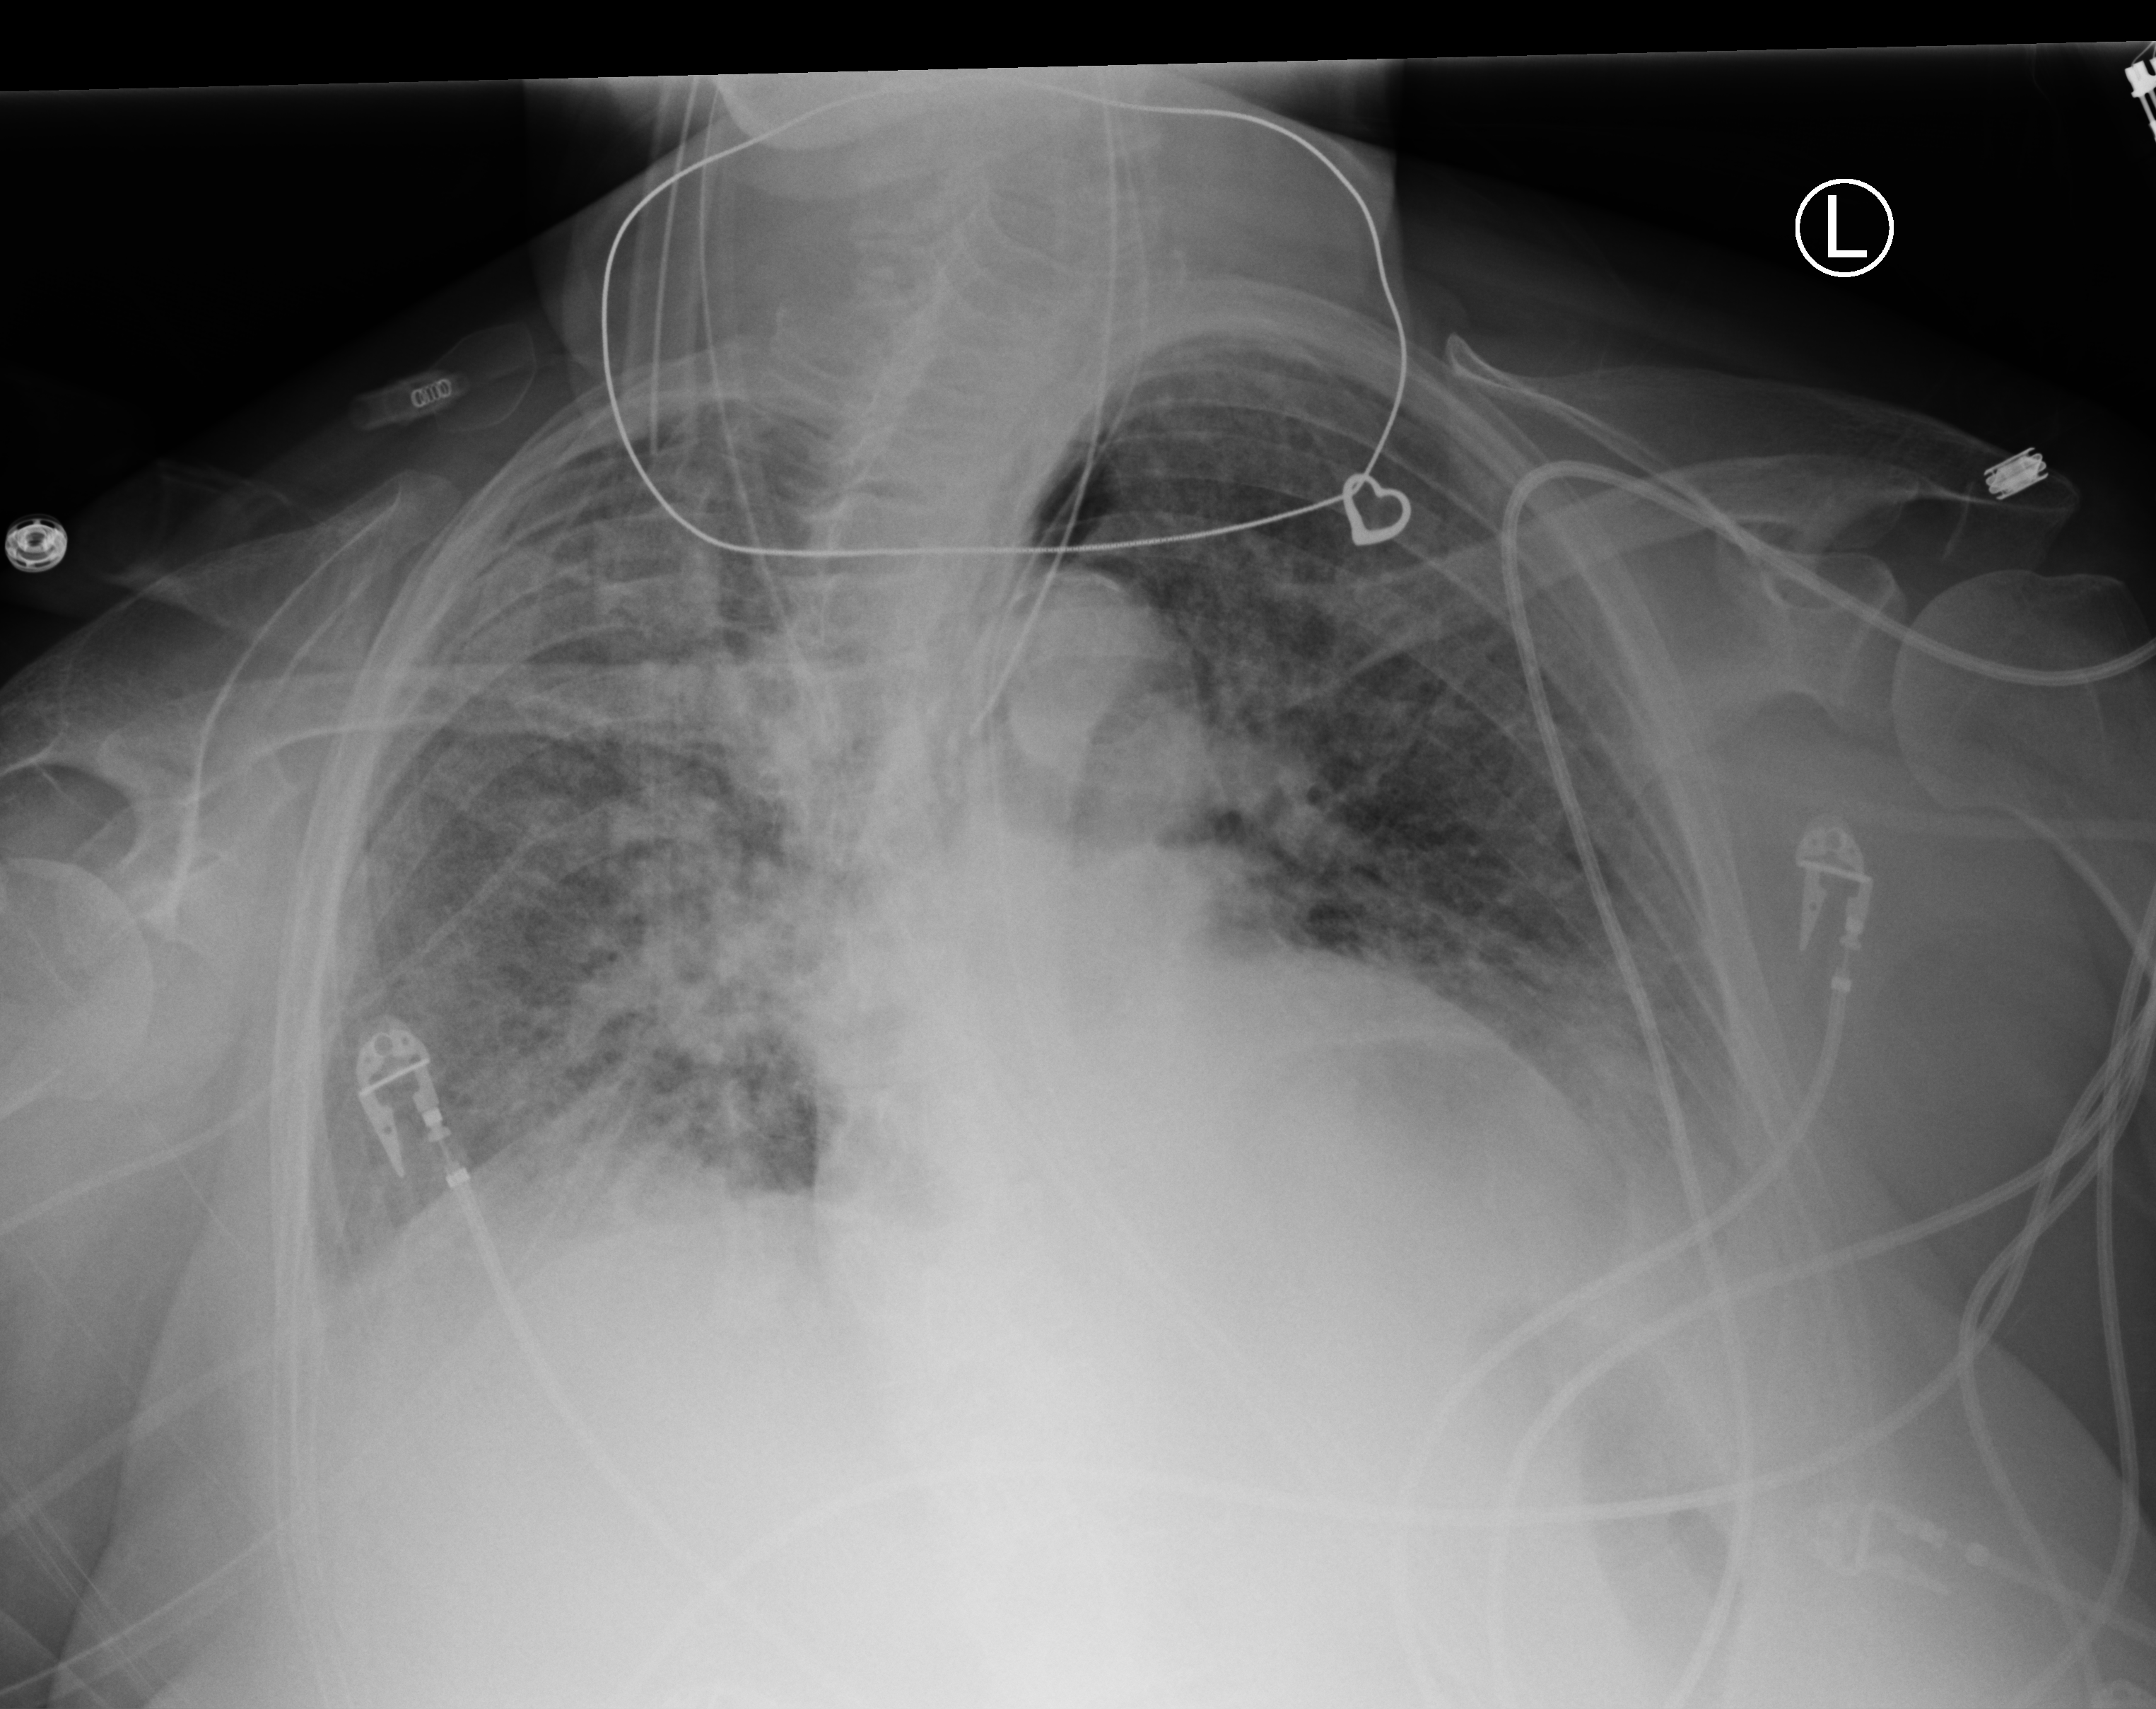
Portable chest radiograph, anteroposterior (AP) projection. Patient hospitalised with COVID-19; female, aged 75–90 years.
Hospital-stay facts (about this admission, not read from this image; timing relative to this image not recorded):
- smoking status (admission record): former
- admitted to intensive care during this hospital stay: yes